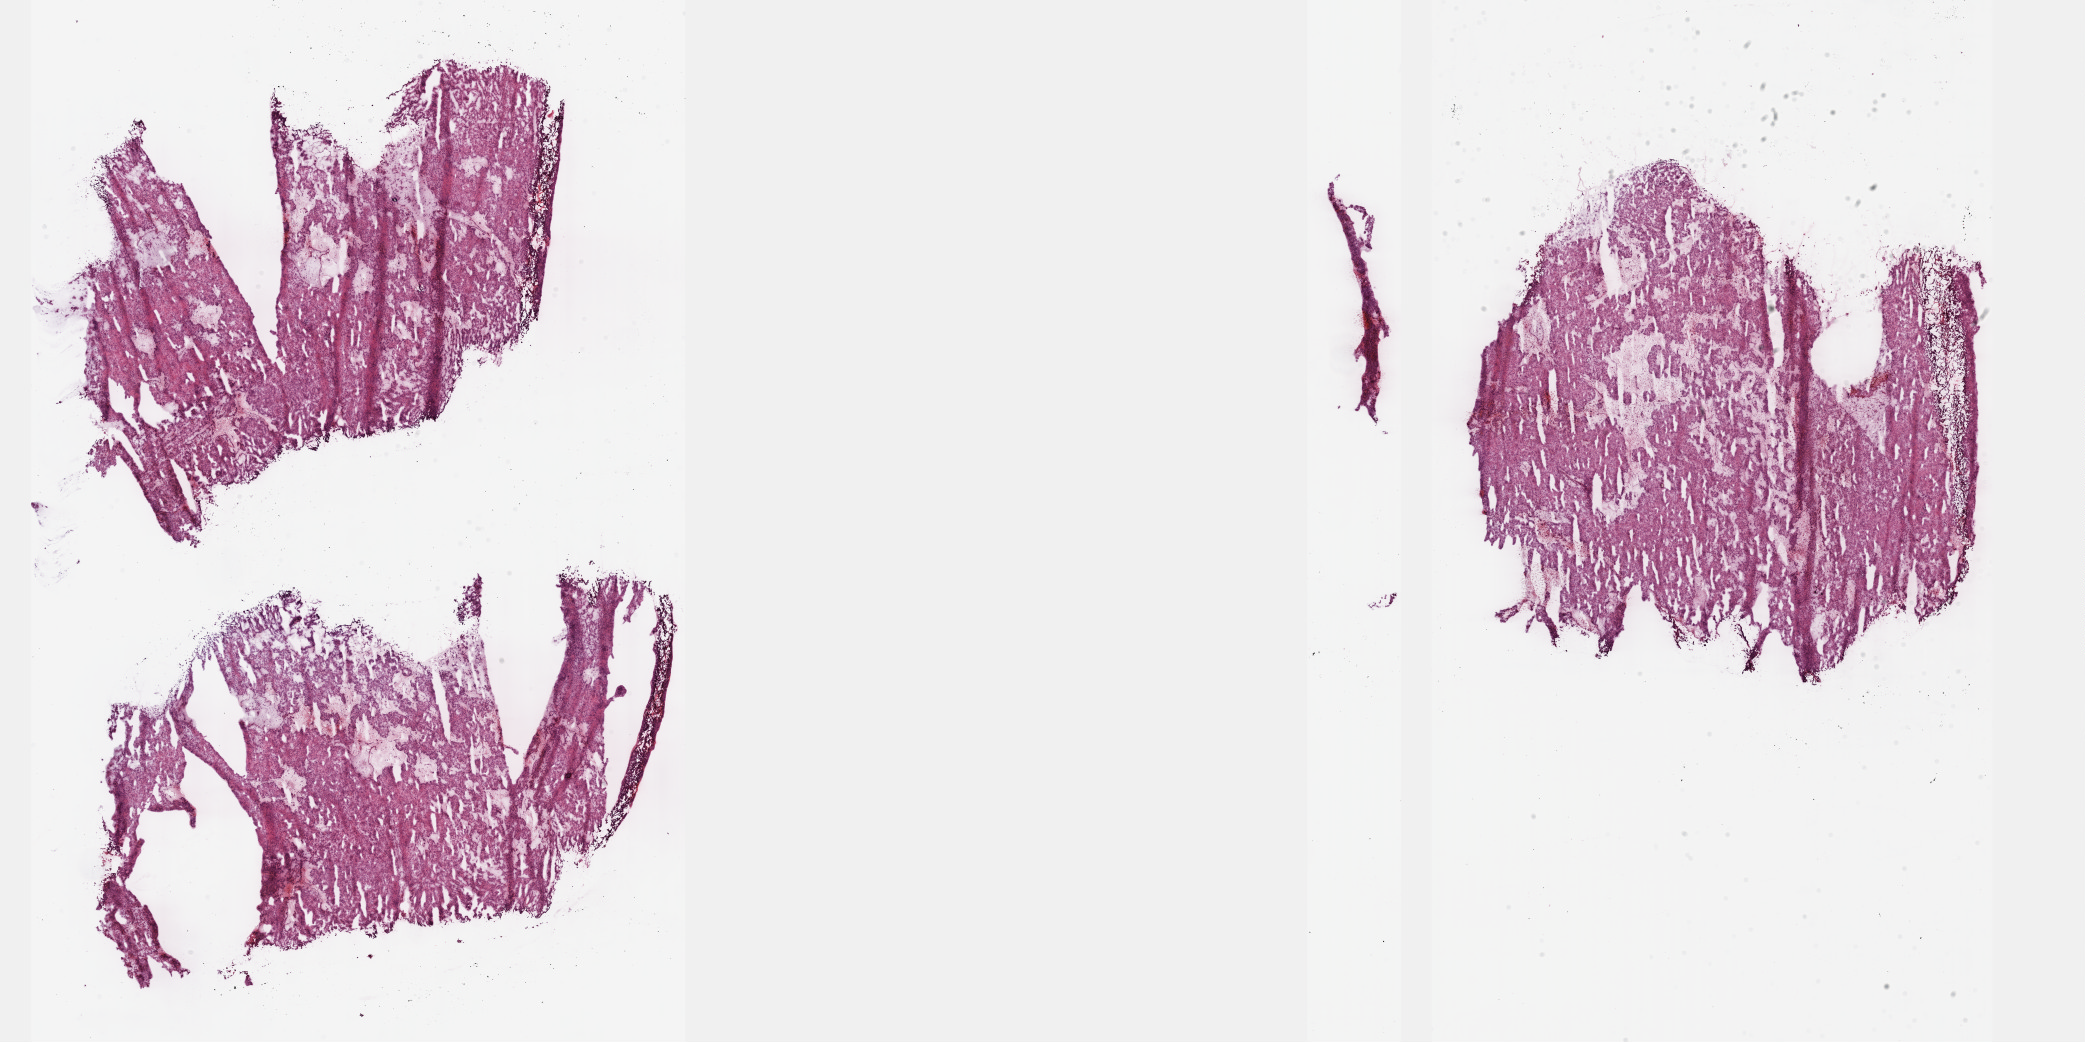
Whole-slide histology image, H&E-stained — a low-resolution overview of the entire scanned area, about 33.7 x 16.8 mm (from a 40x scan). Frozen section from the top of the tissue portion. Sample: primary tumour, adrenal gland. Female, age 73 years at initial diagnosis. Slide review estimates, as recorded: tumour cells 80%, tumour nuclei 80%, normal cells 0%, stromal cells 10%, necrosis 10%. Infiltration values recorded for this section: lymphocyte infiltration 40%, monocyte infiltration 20%, neutrophil infiltration 20%.
Laterality: right. Histologic diagnosis: Pheochromocytoma, malignant.